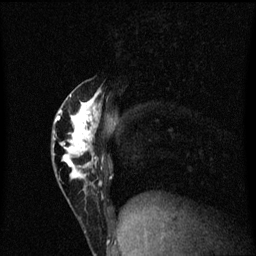
Breast MRI (dynamic contrast-enhanced), one sagittal slice; position 24 of 60 along the scan axis; dynamic contrast-enhanced series, image 2 of 3 at this slice position (ordered by acquisition); 1.5 T; TE 4.2 ms, TR 8.4 ms; 256 × 256 image matrix, field of view 200 × 200 mm. Patient: female, 40 years.
Structures marked on this image (semi-automatically segmented with operator editing):
- analysis volume of interest (the breast-tissue region the enhancement analysis was run in; not a lesion): bounding box (x1, y1, x2, y2) in pixels: (52, 80, 107, 203)
- tumour enhancement mask (voxels above the 70 % enhancement threshold inside the analysis volume of interest): (54, 92, 103, 179)